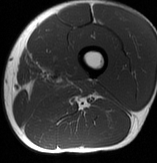
MRI of an extremity soft-tissue mass, one axial slice. Position 18 of 70 along the scan axis. MR volume resampled by the dataset authors to the PET/CT grid (not the native acquisition matrix). 3.27 mm slice thickness. 157 × 163 image matrix, field of view 153 × 159 mm. Male patient. Case-level facts recorded for this patient, not image findings: histological type: extraskeletal osteosarcoma; grade: high; site of the primary tumour: left adductur.
Annotated regions visible in this slice (expert contour drawn on MRI and transferred to this co-registered scan by the dataset authors):
- gross tumour volume (mass): bounding box <51,78,93,96> (left, top, right, bottom; pixels)